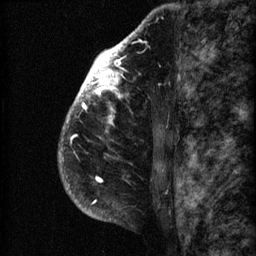
Breast MRI (dynamic contrast-enhanced), one sagittal slice; position 49 of 60 along the scan axis; 3 images stored at this slice position (order not interpretable as contrast timing); 1.5 T; TE 4.2 ms, TR 22.7 ms; 256 × 256 image matrix, field of view 180 × 180 mm. Female patient, age 48 years. From the clinical record (not read from this slice): setting: breast cancer imaged before/during neoadjuvant chemotherapy; receptor status: triple-negative.
Structures marked on this image (semi-automatically segmented with operator editing):
- analysis volume of interest (the breast-tissue region the enhancement analysis was run in; not a lesion): bounding box (x1, y1, x2, y2) in pixels: (58, 30, 173, 207)
- tumour enhancement mask (voxels above the 90 % enhancement threshold inside the analysis volume of interest): (59, 30, 140, 202)